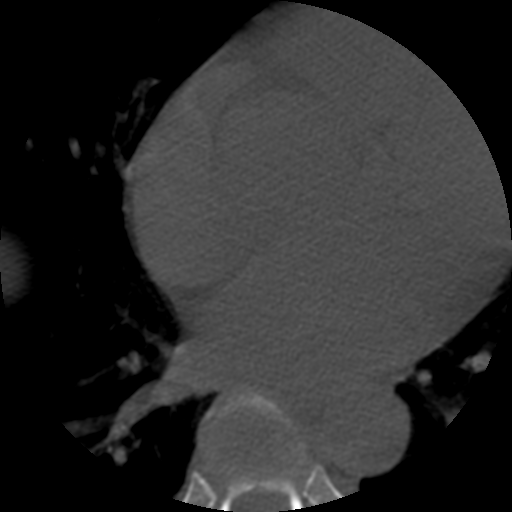
CT including the spine, one axial slice. Slice 342 of 508 in the series (ordered by position). Reconstruction kernel STANDARD. 120 kVp. Bone window (W 1800 / L 400 HU). 1.25 mm slice thickness. 512 × 512 image matrix, field of view 160 × 160 mm. Patient age 57 years. Case-level facts recorded for this patient, not image findings: primary cancer: prostate.
Annotated regions visible in this slice (semi-automatic segmentation, software-assisted and operator-edited):
- T6 vertebra: bounding box (x1, y1, x2, y2) in pixels: (209, 394, 304, 455)
- T7 vertebra: (211, 428, 308, 512)